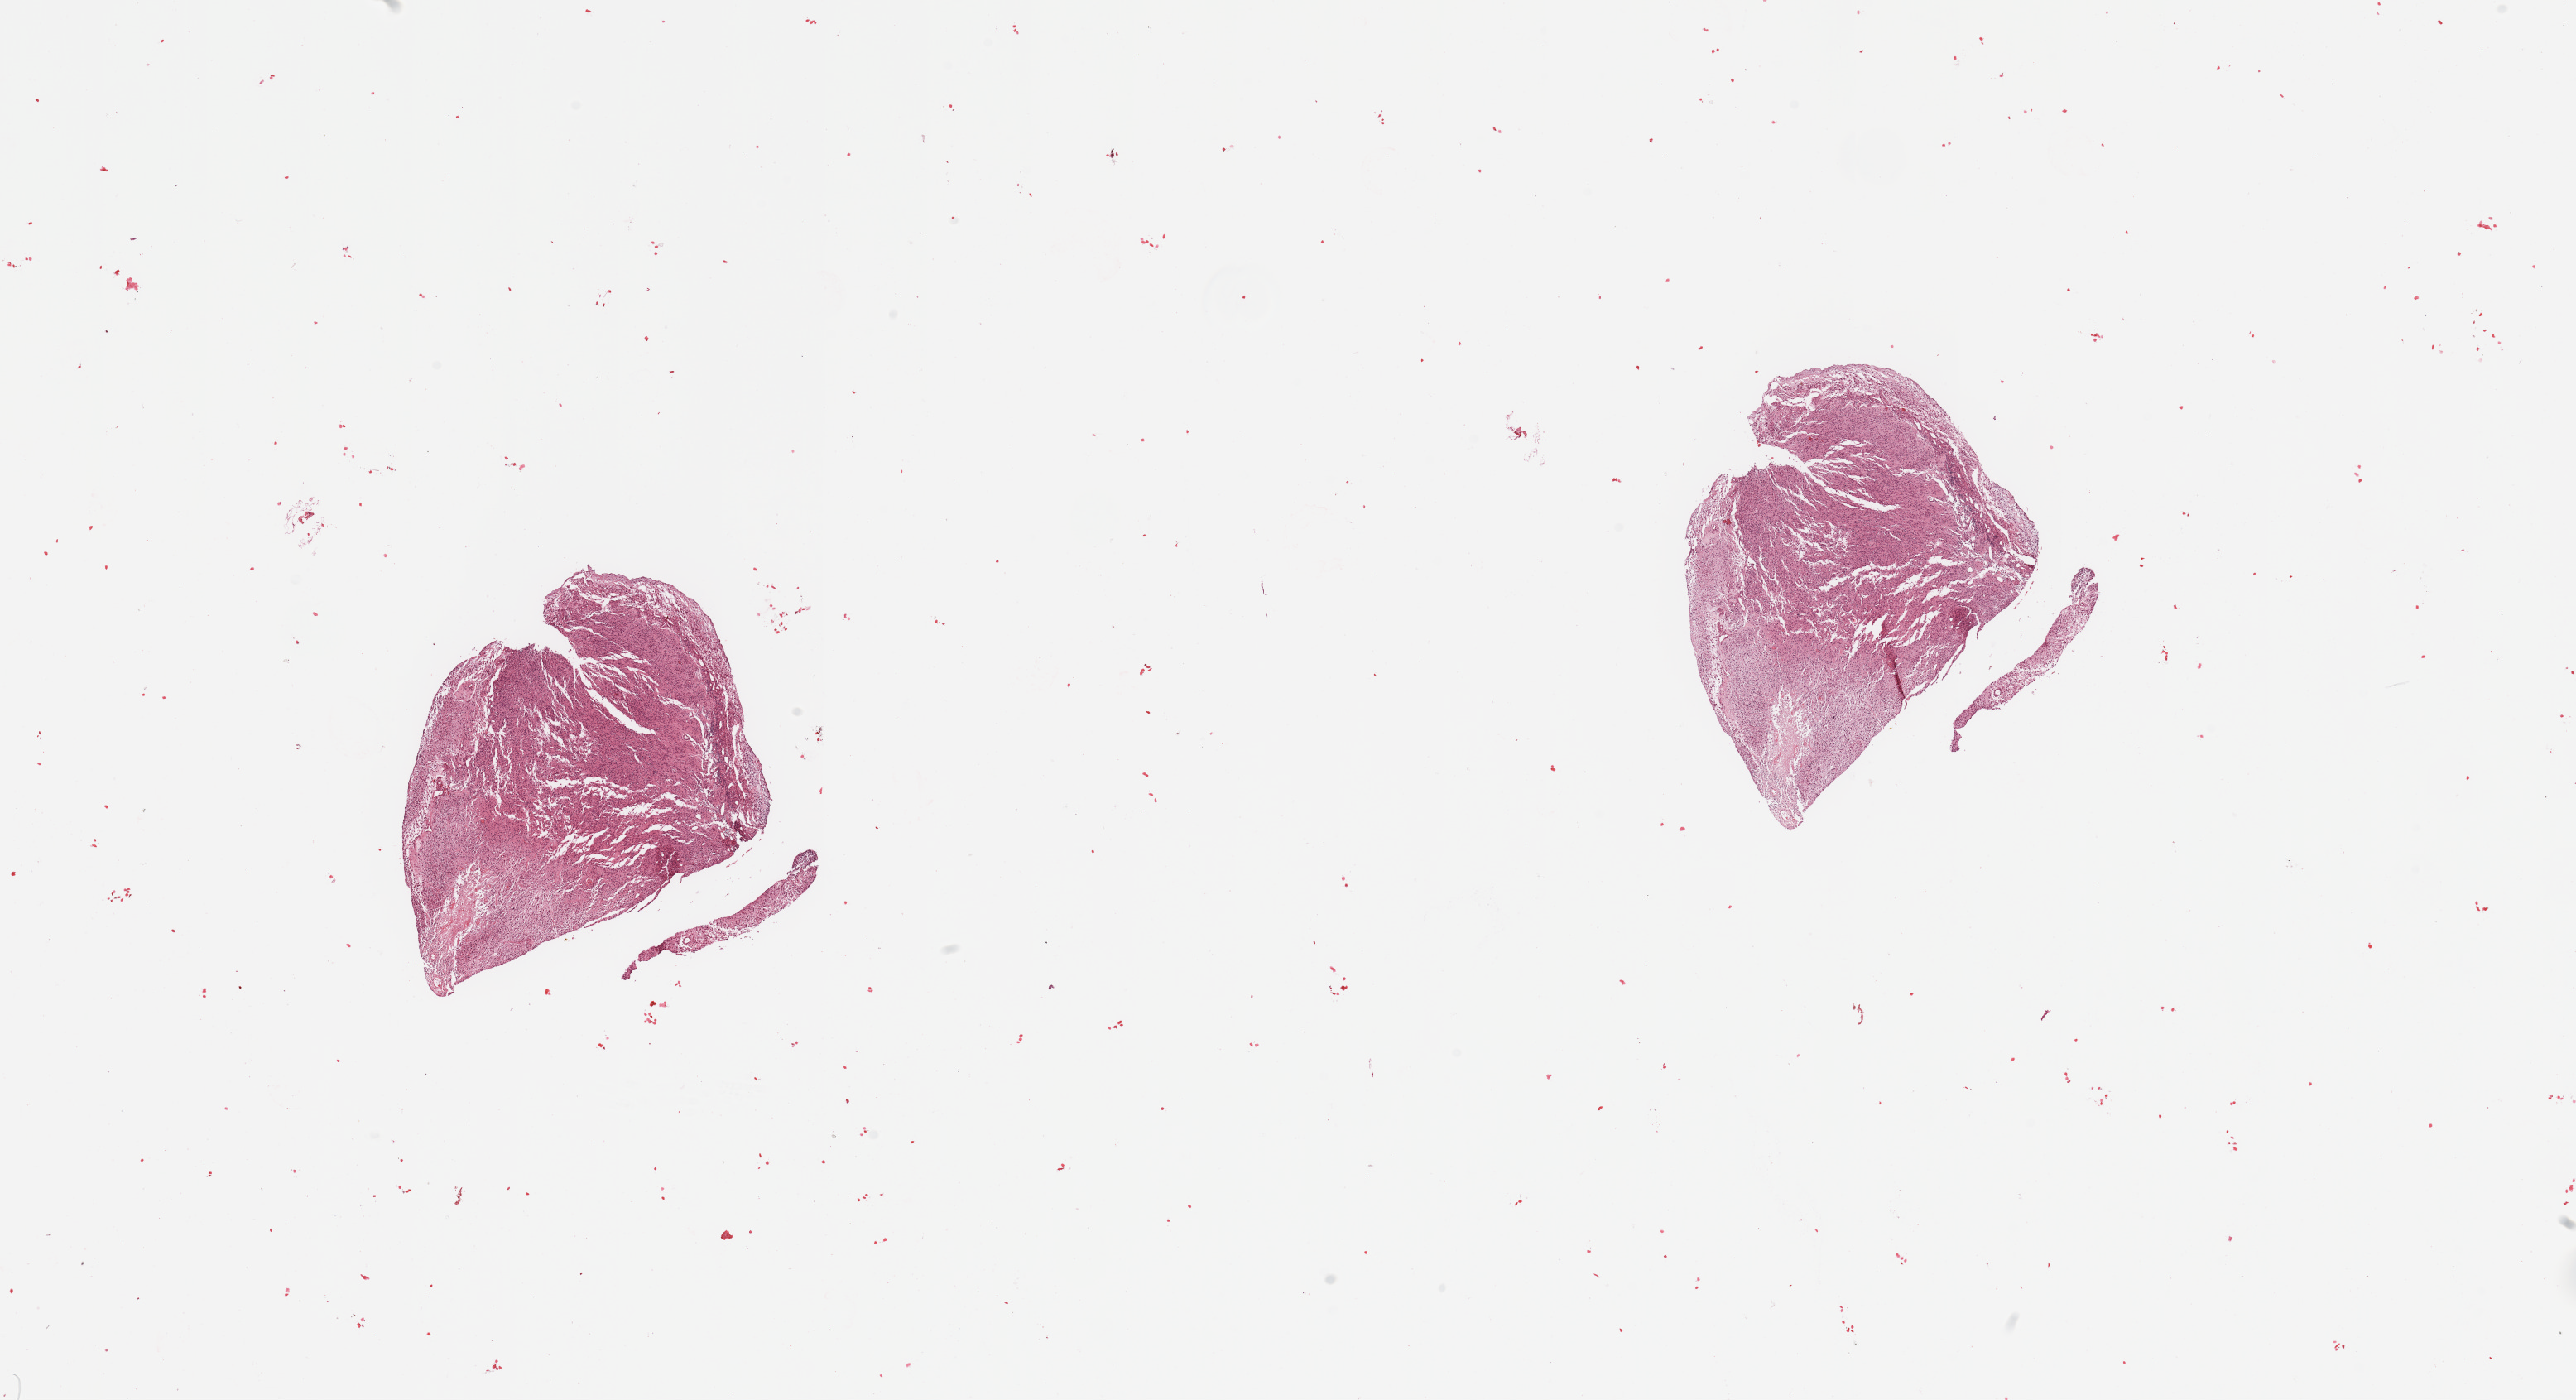
Digitized Hematoxylin and eosin (H&E) stained tissue section (whole slide), whole scanned area (about 24.6 x 13.4 mm) shown as a low-resolution overview. Tumour tissue sample, sampled site: frontal lobe. 60-year-old female patient.
Histologic diagnosis: Glioblastoma.